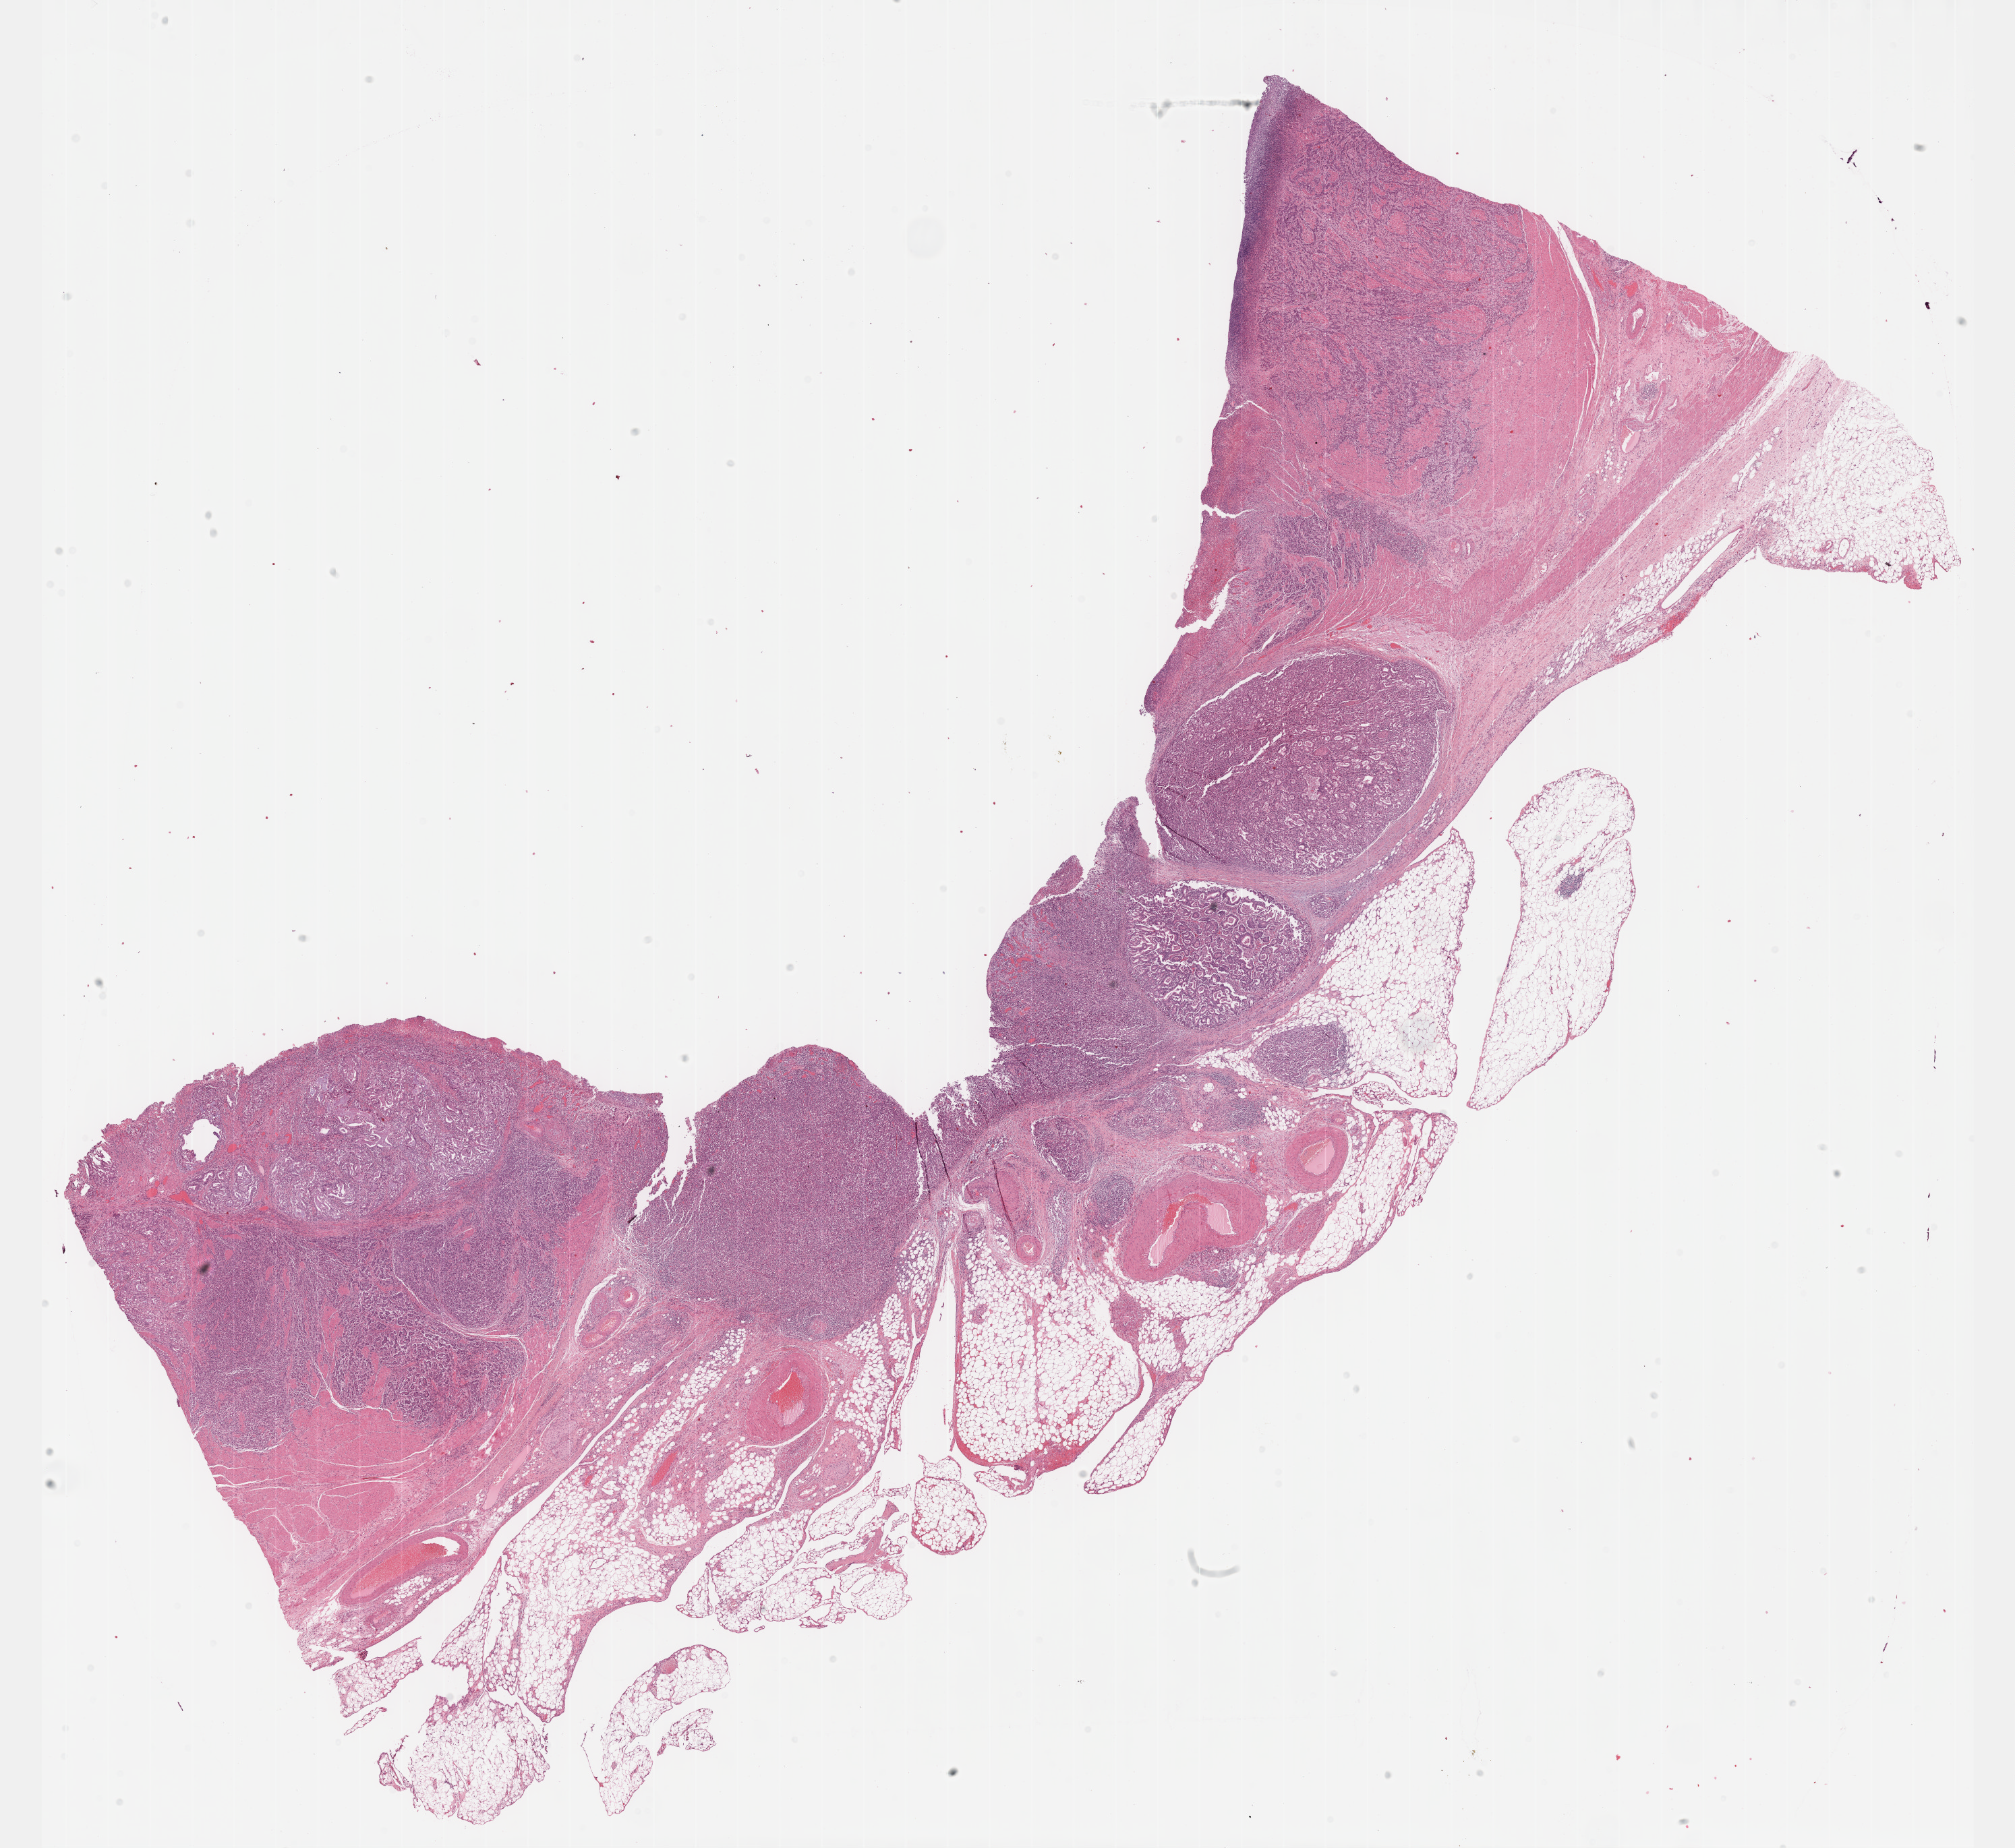
H&E whole-slide image — whole scanned area (about 24.1 x 22.1 mm, from a 40x scan) shown as a low-resolution overview, FFPE section, sample: primary tumour, stomach. Patient: male, age at initial diagnosis 72 years. Histologic grade: G2 (moderately differentiated).
AJCC pathologic stage: IIIA (7th edition). Histologic diagnosis: Tubular adenocarcinoma (body of stomach). Lymph nodes positive (case pathology): 1 of 14 examined.